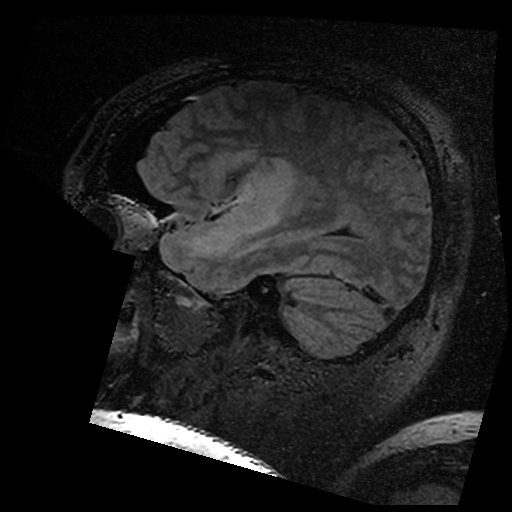
Brain MRI from a brain-tumour surgery series, one sagittal slice. Position 124 of 176 along the scan axis. T2 FLAIR. 1 mm slice thickness. 512 × 512 image matrix, field of view 250 × 250 mm. Case-level facts recorded for this patient, not image findings: histopathology: Astrocytoma; WHO grade: 3; IDH mutation: yes.
Structures marked on this image (expert manual segmentation):
- residual tumour: bounding box [x1, y1, x2, y2] px = [211, 146, 293, 201]